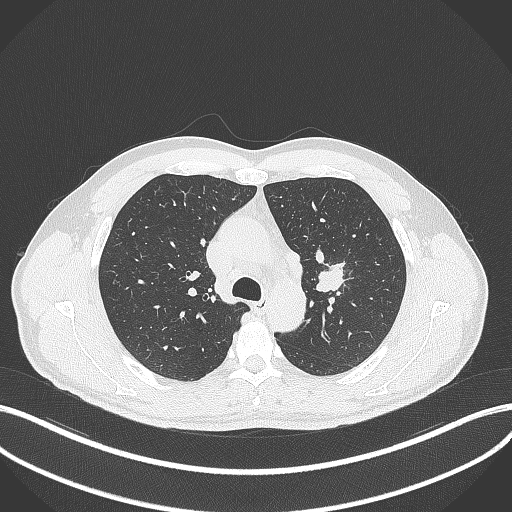
Chest CT, one axial slice. Slice 294 of 392 in the series (ordered by position). Reconstruction kernel B70f. 120 kVp. Lung window (W 1500 / L -600 HU). 1 mm slice thickness. 512 × 512 image matrix, field of view 400 × 400 mm. Patient: male, 50 years. Case-level facts recorded for this patient, not image findings: clinical TNM (as recorded): T1c N1 M1b.
Structures marked on this image (rectangle marked by the reading radiologist):
- lung tumour (recorded histology: squamous cell carcinoma): box from (x=314, y=255) to (x=349, y=296) px